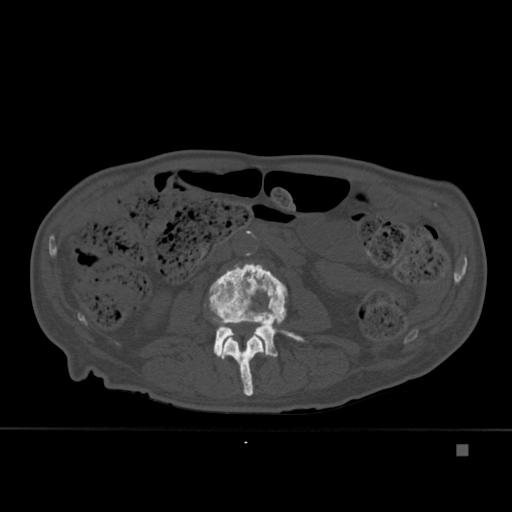
CT including the spine, one axial slice; position 150 of 451 along the scan axis; bone window (W 1800 / L 400 HU); 1.5 mm slice thickness; 512 × 512 image matrix, field of view 378 × 378 mm. Patient: male, 75 years. Case-level facts recorded for this patient, not image findings: primary cancer: prostate.
Structures marked on this image (semi-automatically segmented with operator editing):
- L2 vertebra: bounding box [x1, y1, x2, y2] px = [221, 336, 265, 397]
- L3 vertebra: [204, 262, 305, 358]